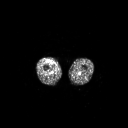
FDG PET of an extremity soft-tissue mass (from a PET/CT study), one axial slice. Position 224 of 311 along the scan axis. 3.27 mm slice thickness. 128 × 128 image matrix. Patient: male, 56 years. From the clinical record (not read from this slice): histological type: pleiomorphic leiomyosarcoma; grade: intermediate; site of the primary tumour: right thigh.
Outlined on this slice (expert contour drawn on MRI and transferred to this co-registered scan by the dataset authors):
- gross tumour volume including surrounding oedema: bounding box [x1, y1, x2, y2] px = [47, 60, 51, 62]